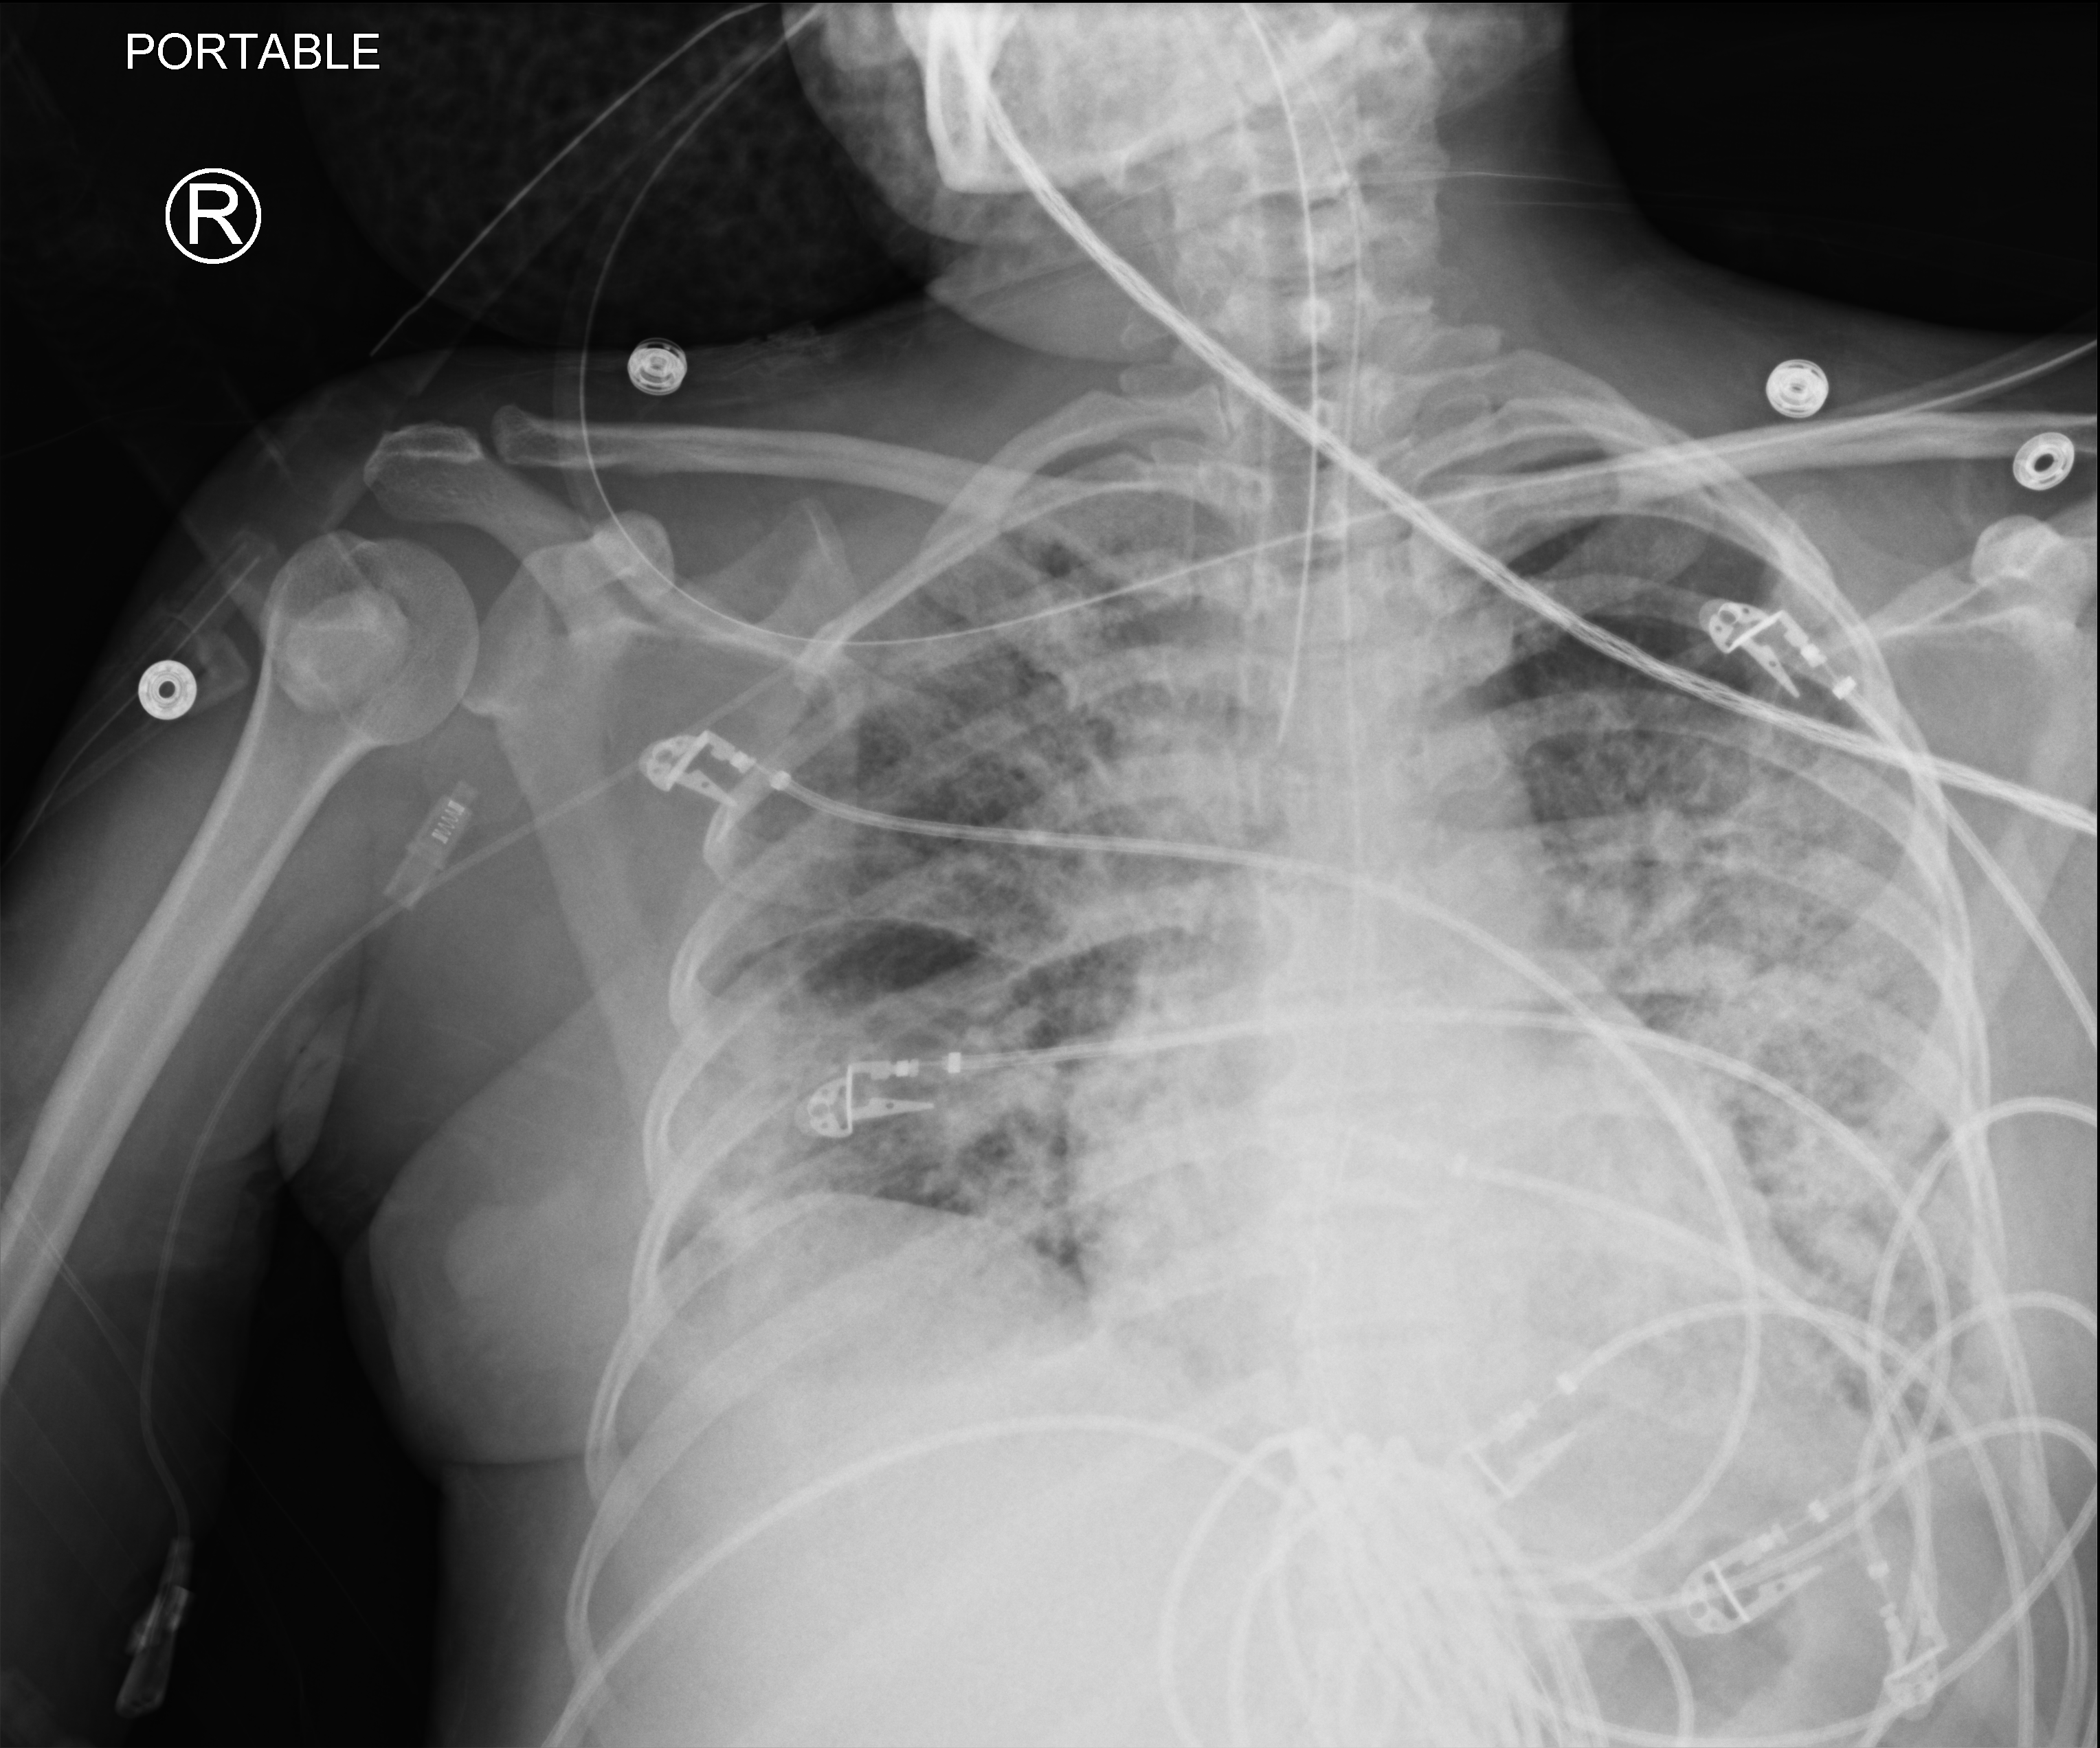
Portable chest radiograph; anteroposterior (AP) projection. Patient hospitalised with COVID-19; female, aged 18–59 years.
Hospital-stay facts (about this admission, not read from this image; timing relative to this image not recorded): mechanically ventilated during this hospital stay: yes.